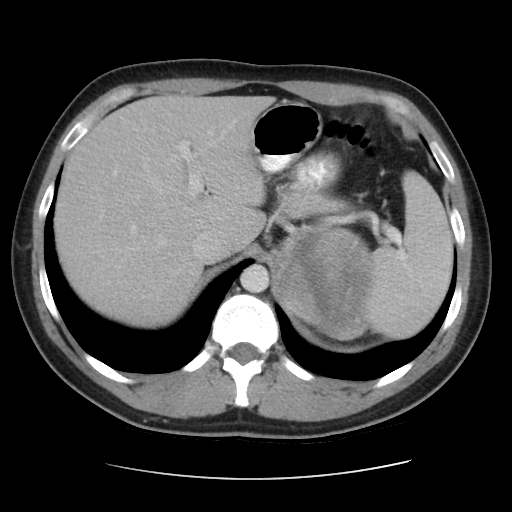
Contrast-enhanced abdominal CT, one axial slice; slice 34 of 48 in the series (ordered by position); reconstruction kernel STANDARD; 120 kVp; intravenous contrast given; soft-tissue window (W 400 / L 40 HU); 5 mm slice thickness; 512 × 512 image matrix, field of view 360 × 360 mm. Patient: male, 32 years. From the clinical record (not read from this slice): diagnosis: adrenocortical carcinoma; tumour side: left adrenal.
Outlined on this slice (semi-automatic segmentation, software-assisted and operator-edited):
- mass: bounding box [x1, y1, x2, y2] px = [279, 231, 370, 336]